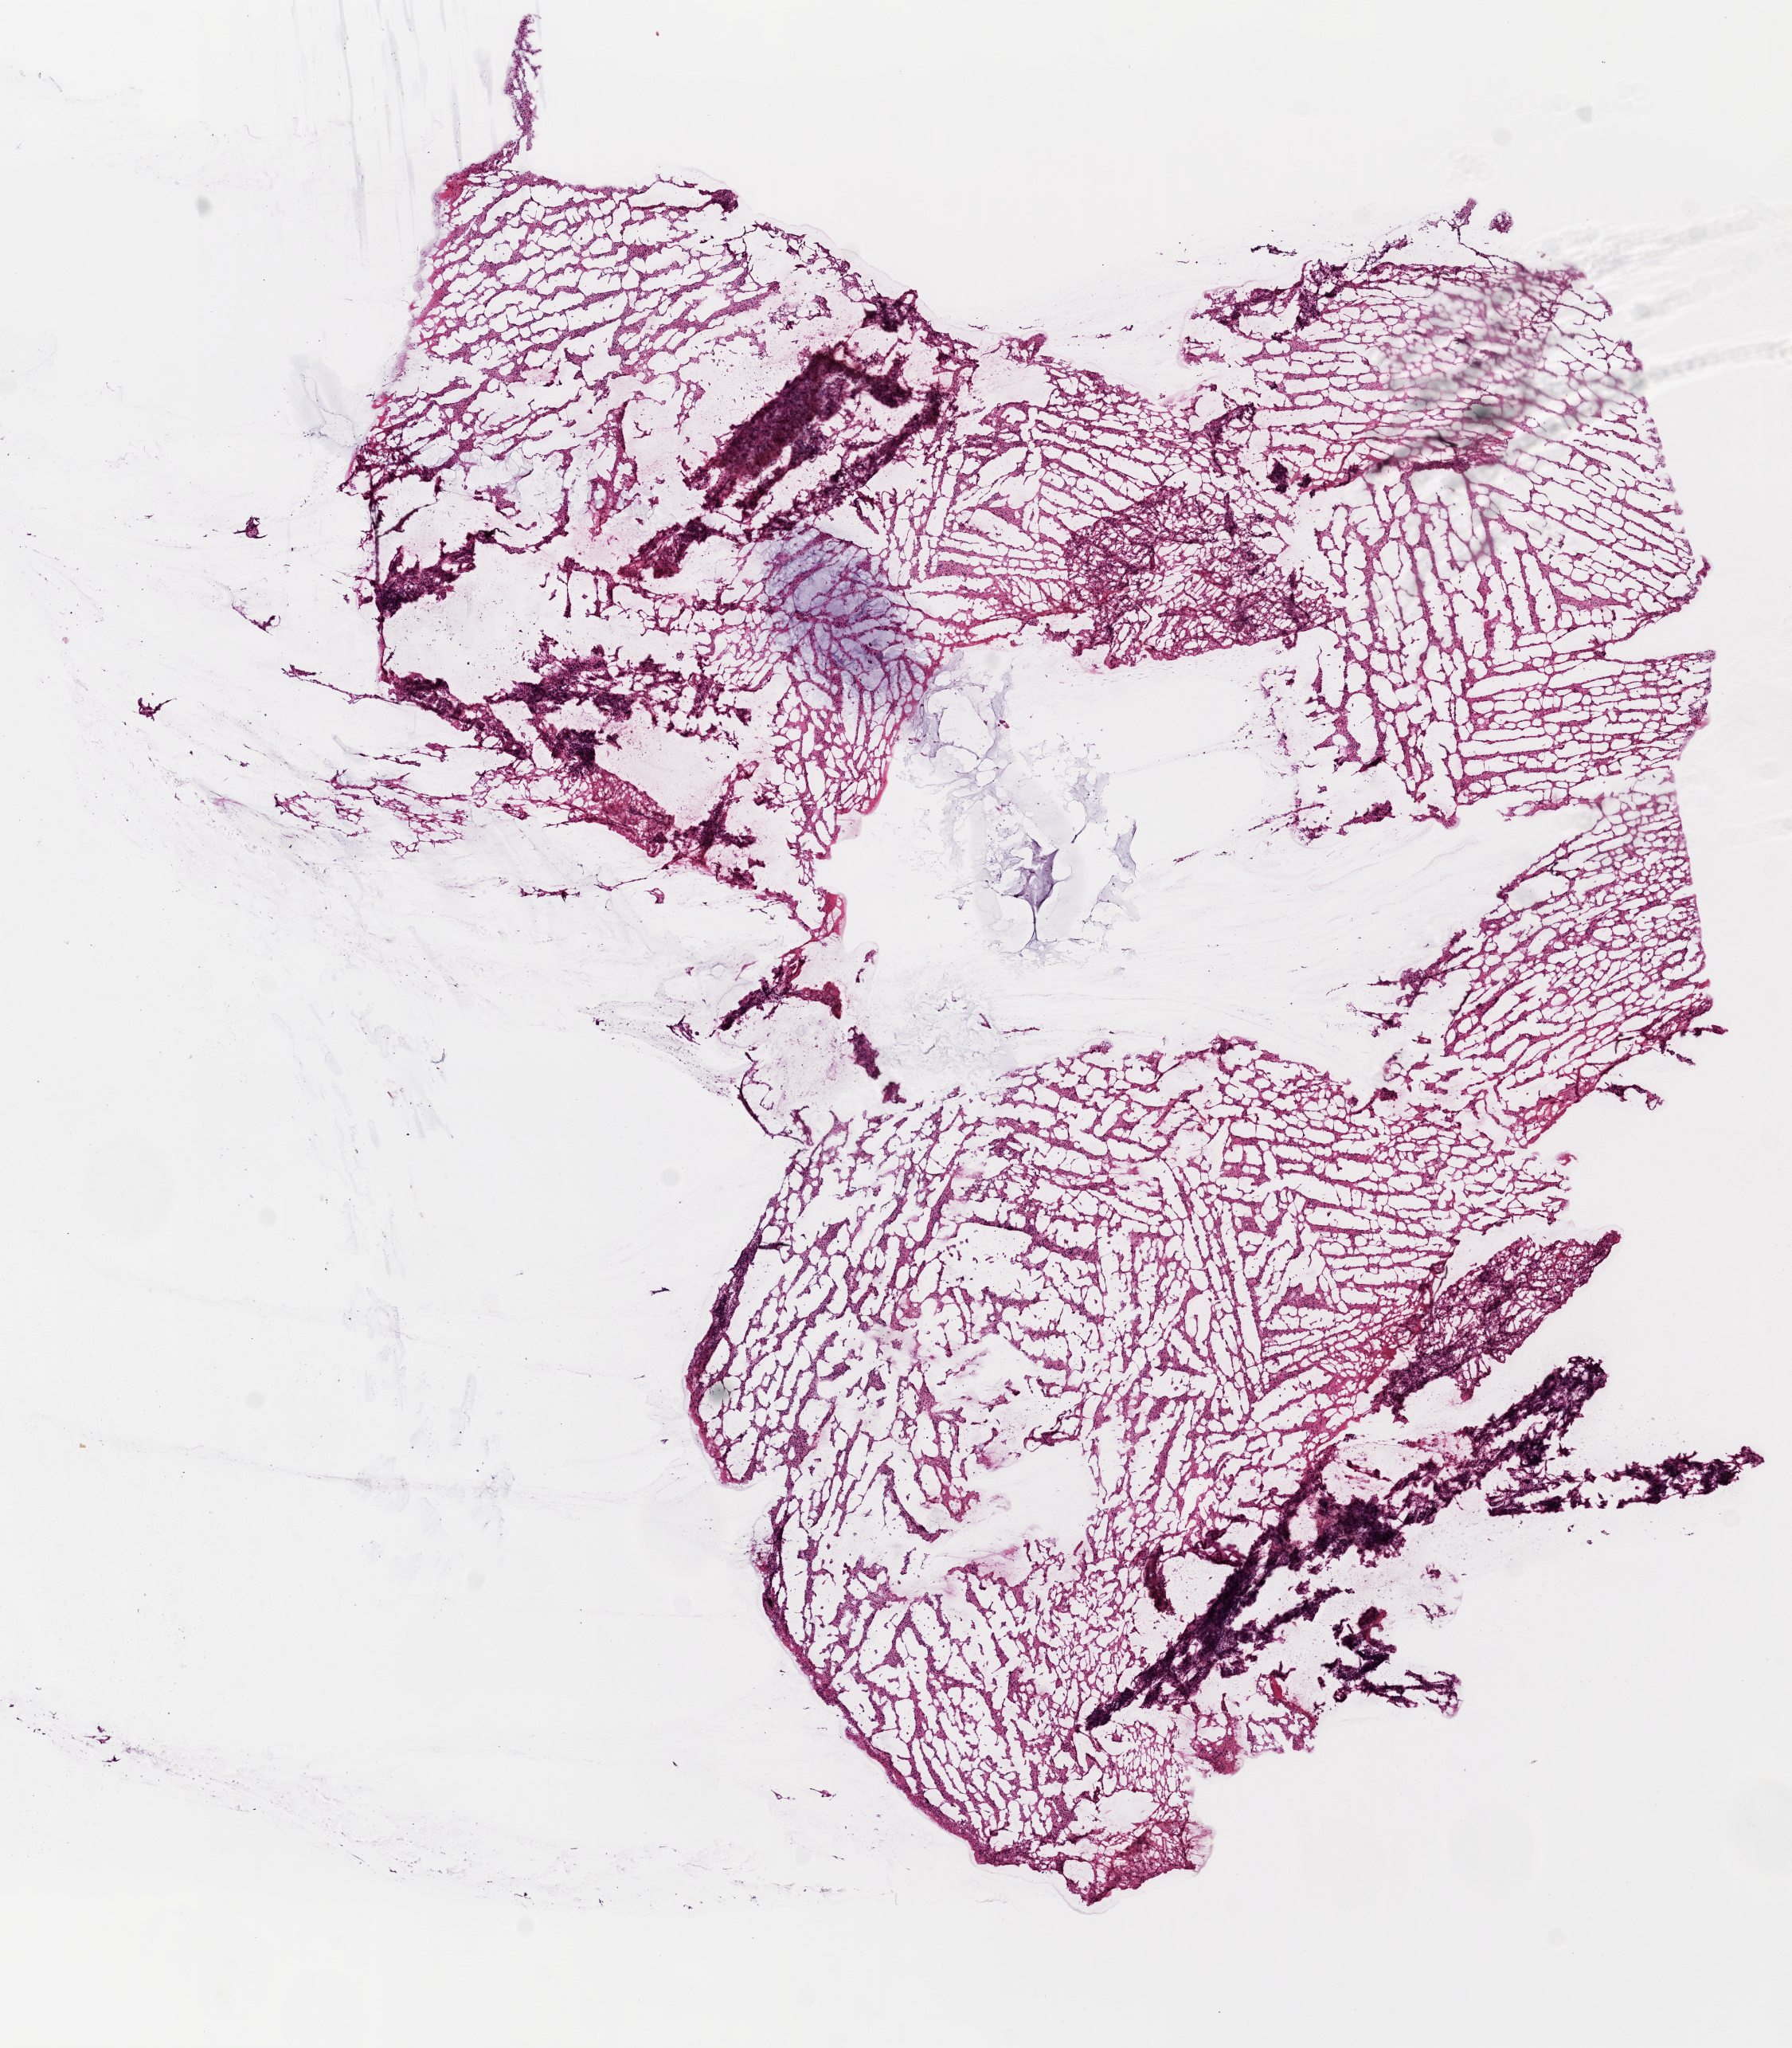
Whole-slide histology image, H&E, whole scanned area (about 9.0 x 10.3 mm) shown as a low-resolution overview; frozen section from the top of the tissue portion; brain, primary tumour sample. Patient: female, age at initial diagnosis 56 years. Histologic grade: G3 (poorly differentiated). Composition of this section per pathologist review: tumour cells 100%, tumour nuclei 75%, normal cells 0%, stromal cells 0%, necrosis 0%.
• pathologic diagnosis: Oligodendroglioma, anaplastic